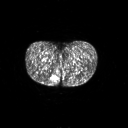
FDG PET of an extremity soft-tissue mass (from a PET/CT study), one axial slice; slice 16 of 267 in the series (ordered by position); 3.27 mm slice thickness; 128 × 128 image matrix. Female patient, age 17 years. From the clinical record (not read from this slice): histological type: epithelioid sarcoma; grade: intermediate; site of the primary tumour: right buttock.
Structures marked on this image (expert contour drawn on MRI and transferred to this co-registered scan by the dataset authors):
- gross tumour volume including surrounding oedema: bounding box <51,75,60,87> (left, top, right, bottom; pixels)
- gross tumour volume (mass): <54,77,56,80>